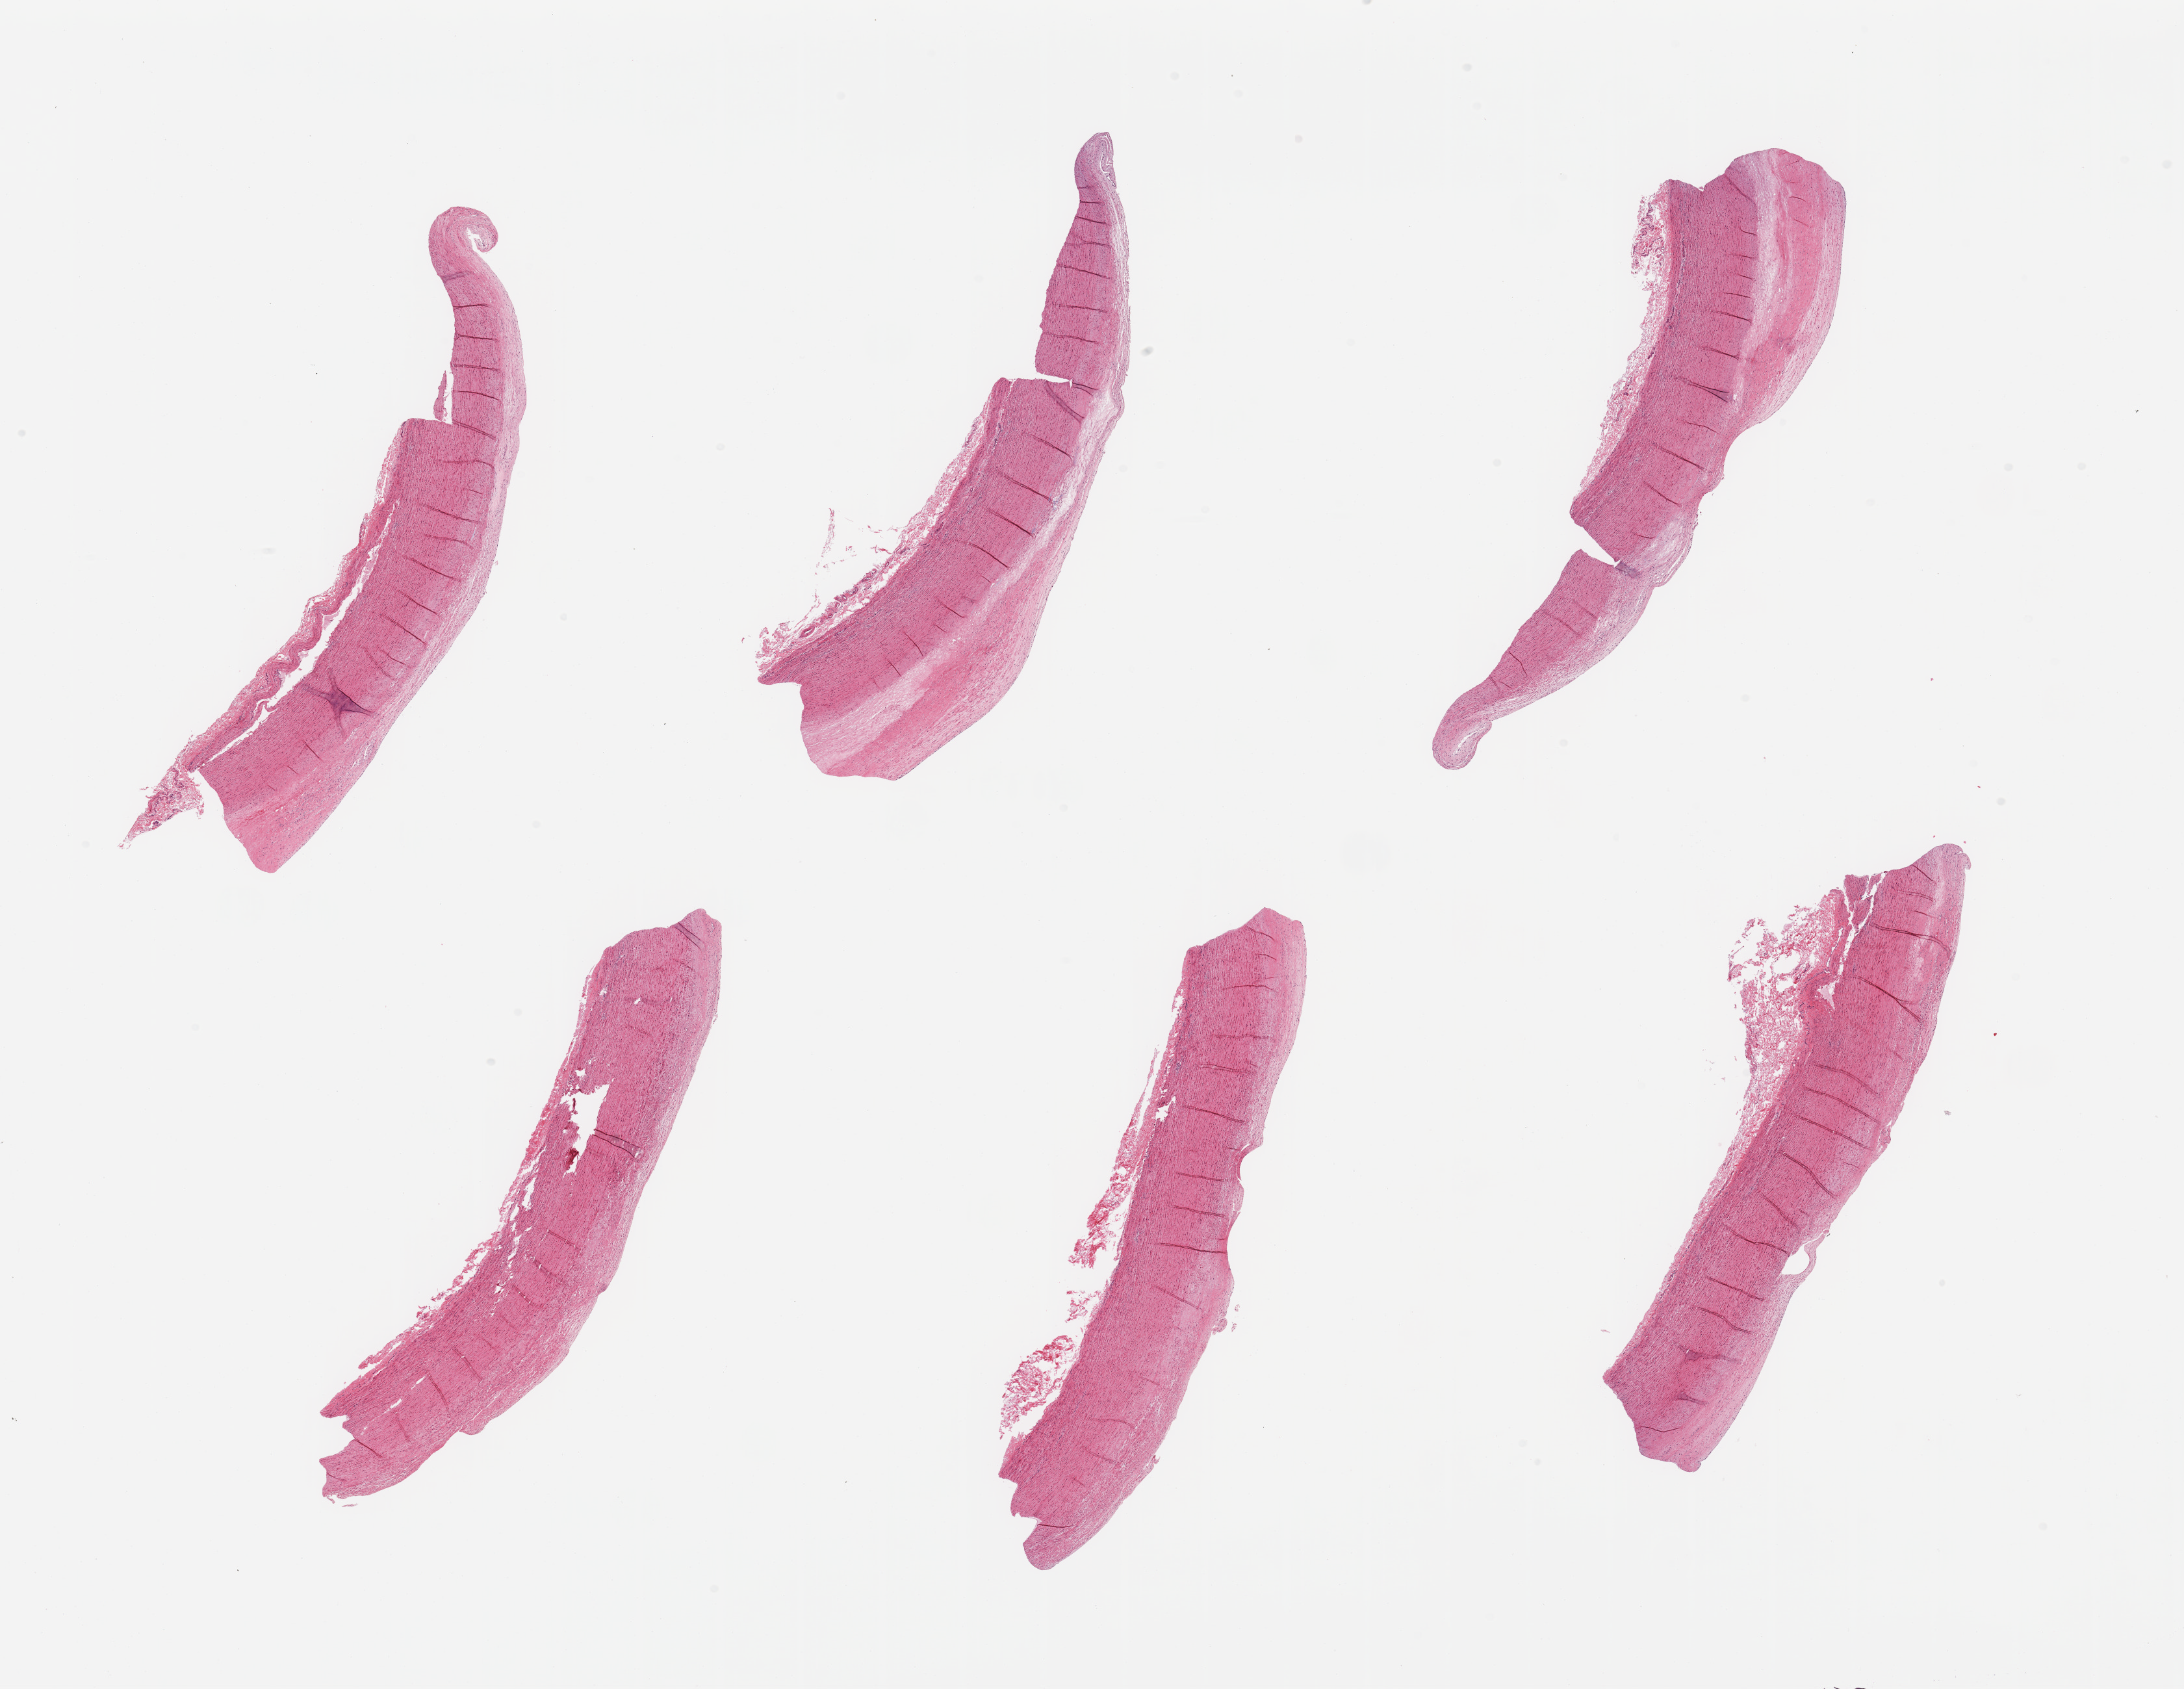
Digitized hematoxylin and eosin (H&E)-stained section, a low-resolution overview of the entire scanned area, about 26.6 x 20.6 mm, PAXgene-fixed paraffin-embedded (PFPE) section, target tissue: aorta, donor tissue sample. Donor sex: male.
Pathologist's review note for this sample: 6 pieces; flat atheromatous plaques up to 1 mm thick.